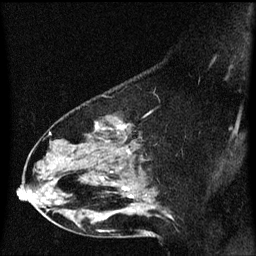
Breast MRI (dynamic contrast-enhanced), one sagittal slice. Position 38 of 60 along the scan axis. Dynamic contrast-enhanced series, image 2 of 3 at this slice position (ordered by acquisition). 1.5 T. TE 4.2 ms, TR 8.4 ms. 256 × 256 image matrix, field of view 200 × 200 mm. Patient: female, 49 years. Case-level facts recorded for this patient, not image findings: setting: breast cancer imaged before/during neoadjuvant chemotherapy; receptor status: HR-positive, HER2-negative.
Annotated regions visible in this slice (semi-automatically segmented with operator editing):
- analysis volume of interest (the breast-tissue region the enhancement analysis was run in; not a lesion): bounding box (x1, y1, x2, y2) in pixels: (27, 96, 174, 221)
- tumour enhancement mask (voxels above the 70 % enhancement threshold inside the analysis volume of interest): (118, 122, 133, 197)